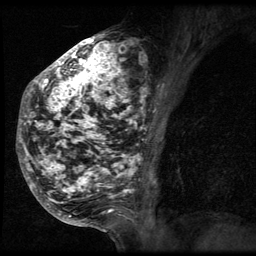
Breast MRI (dynamic contrast-enhanced), one sagittal slice; position 28 of 64 along the scan axis; 3 images stored at this slice position (order not interpretable as contrast timing); 1.5 T; TE 4.2 ms, TR 9 ms; 2.5 mm slice thickness; 256 × 256 image matrix. Patient: female, 50 years. Case-level facts recorded for this patient, not image findings: setting: breast cancer imaged before/during neoadjuvant chemotherapy; receptor status: triple-negative.
Outlined on this slice (semi-automatically segmented with operator editing):
- analysis volume of interest (the breast-tissue region the enhancement analysis was run in; not a lesion): bounding box [x1, y1, x2, y2] px = [24, 39, 148, 212]
- tumour enhancement mask (voxels above the 140 % enhancement threshold inside the analysis volume of interest): [24, 39, 148, 211]